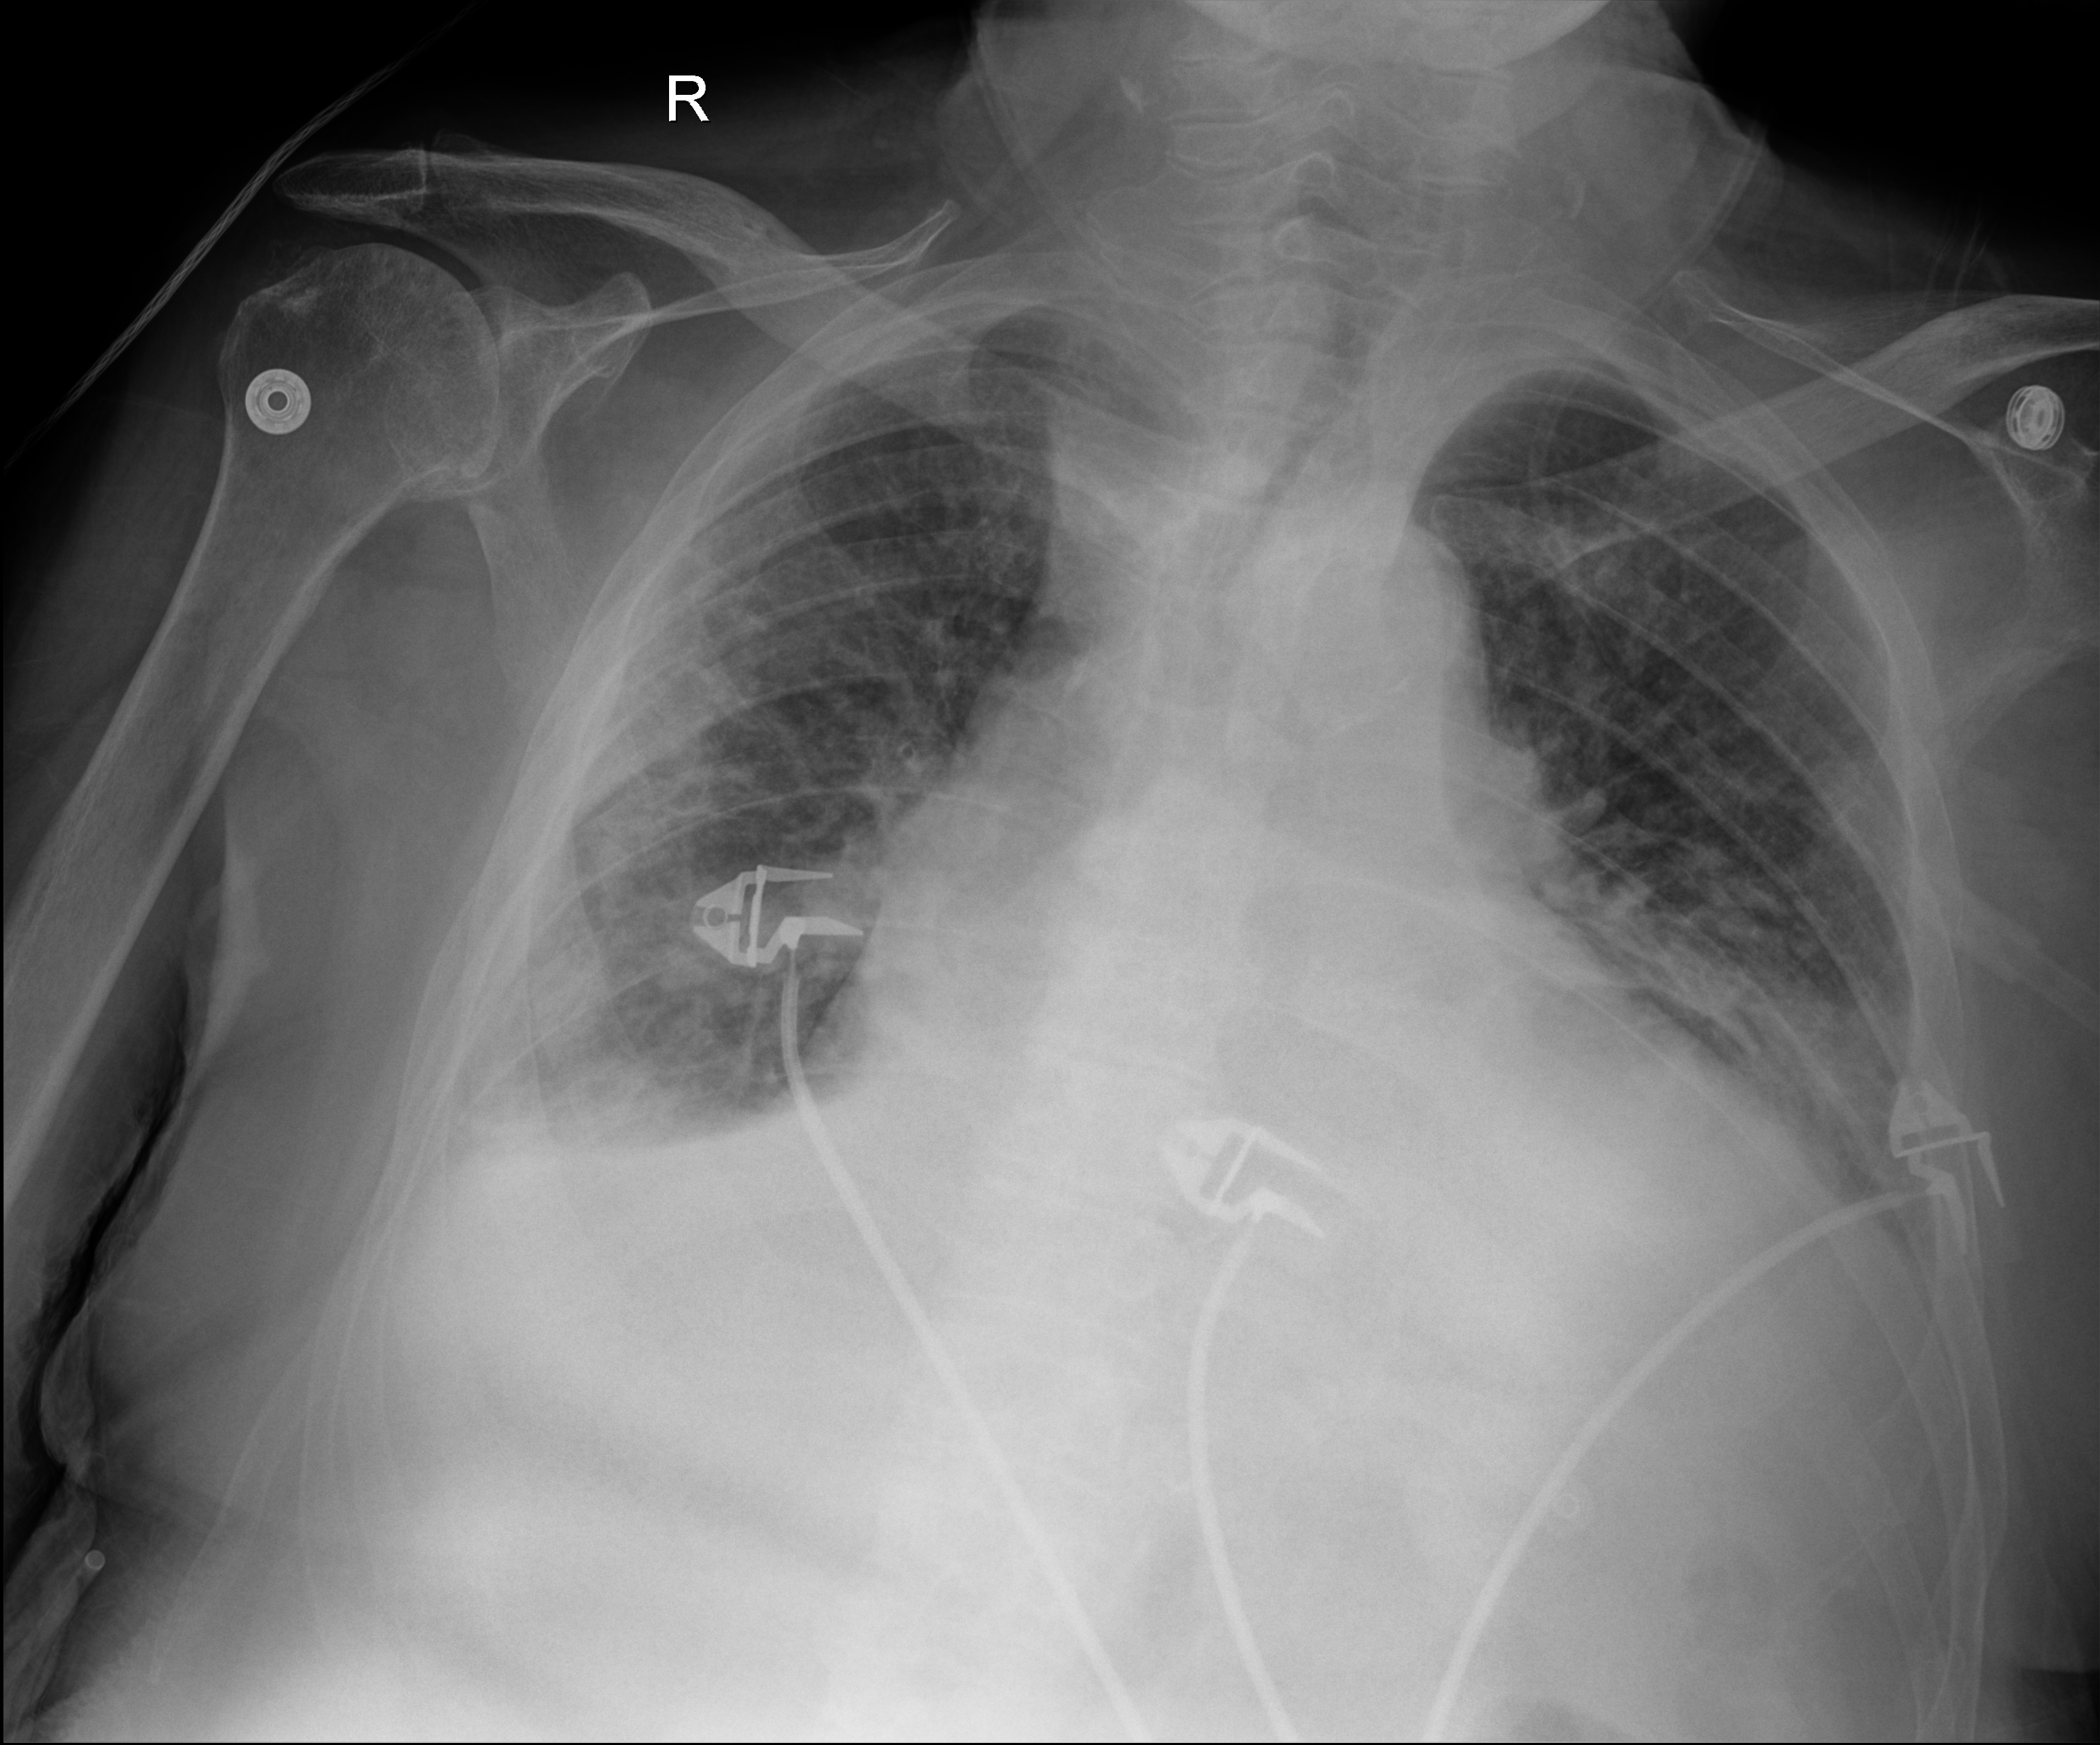
Portable chest radiograph; anteroposterior (AP) projection. Male patient hospitalised with COVID-19, age 75–90 years.
Admission-level facts for this patient (not findings on this image; timing relative to this image not recorded): length of hospital stay: 20 days; COPD (admission record): no; hypertension (admission record): yes.